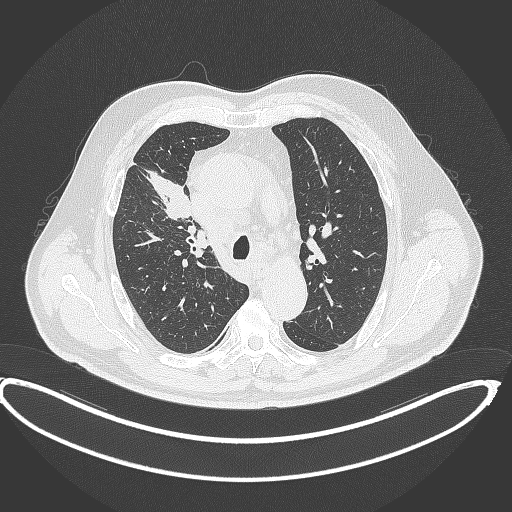
Chest CT, one axial slice. 120 kVp. Lung window (W 1500 / L -600 HU). 1 mm slice thickness. 512 × 512 image matrix, field of view 448 × 448 mm. Patient: male, 62 years. Case-level facts recorded for this patient, not image findings: clinical TNM (as recorded): T1c N3 M1c.
Annotated regions visible in this slice (bounding box drawn by a radiologist):
- lung tumour (recorded histology: adenocarcinoma): bounding box <144,166,194,221> (left, top, right, bottom; pixels)